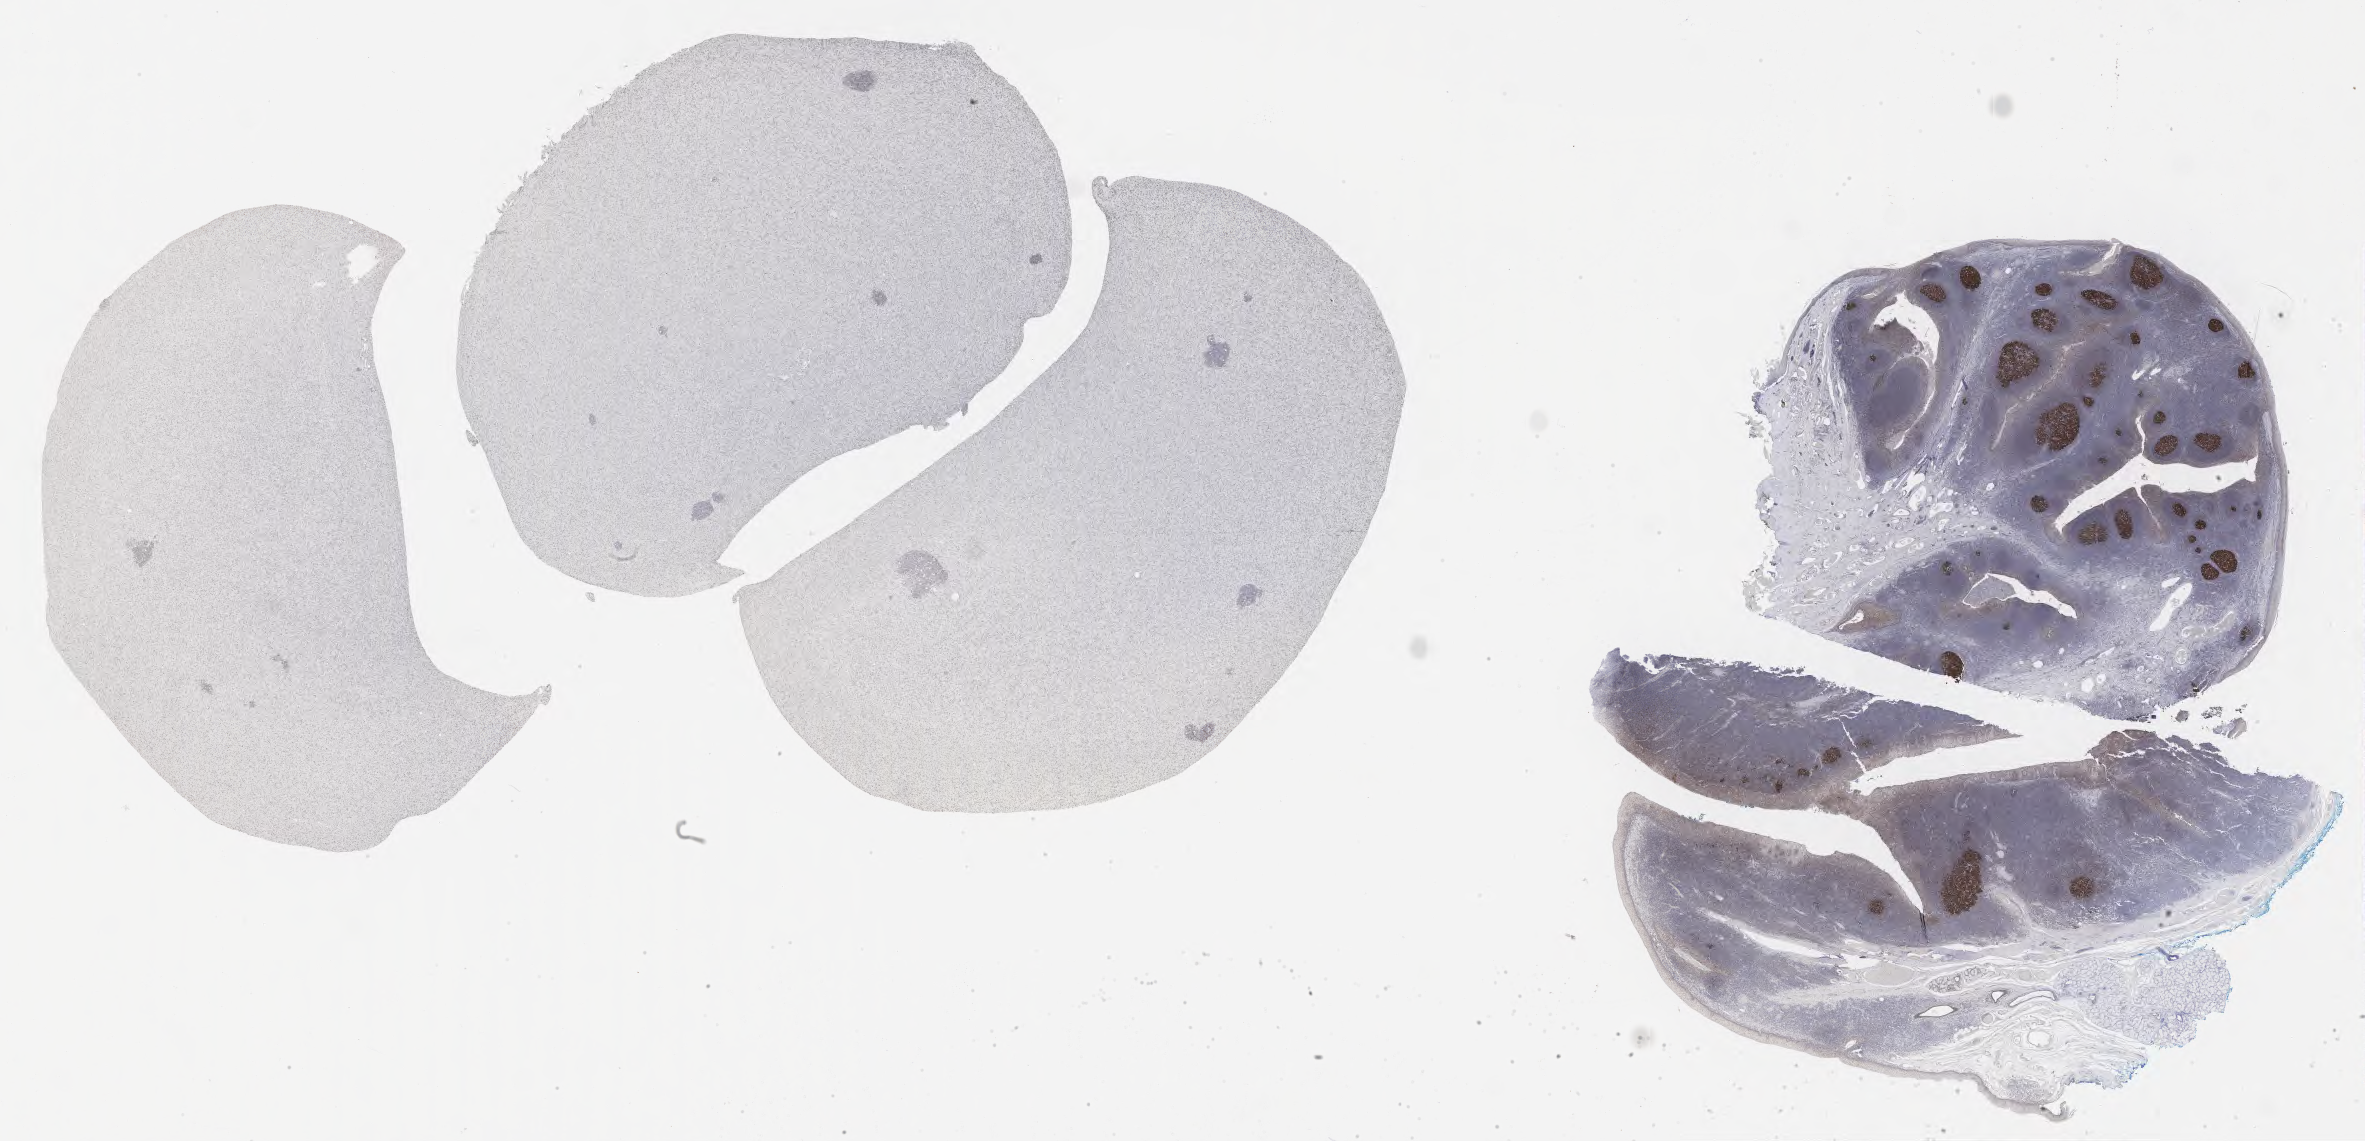
Immunohistochemistry (IHC) whole-slide image stained for BCL6 — low-resolution overview of the scanned area, about 38.2 x 18.4 mm. Specimen: tumor tissue. Patient: male, age 17 years.
Histologic diagnosis: Burkitt lymphoma, NOS.